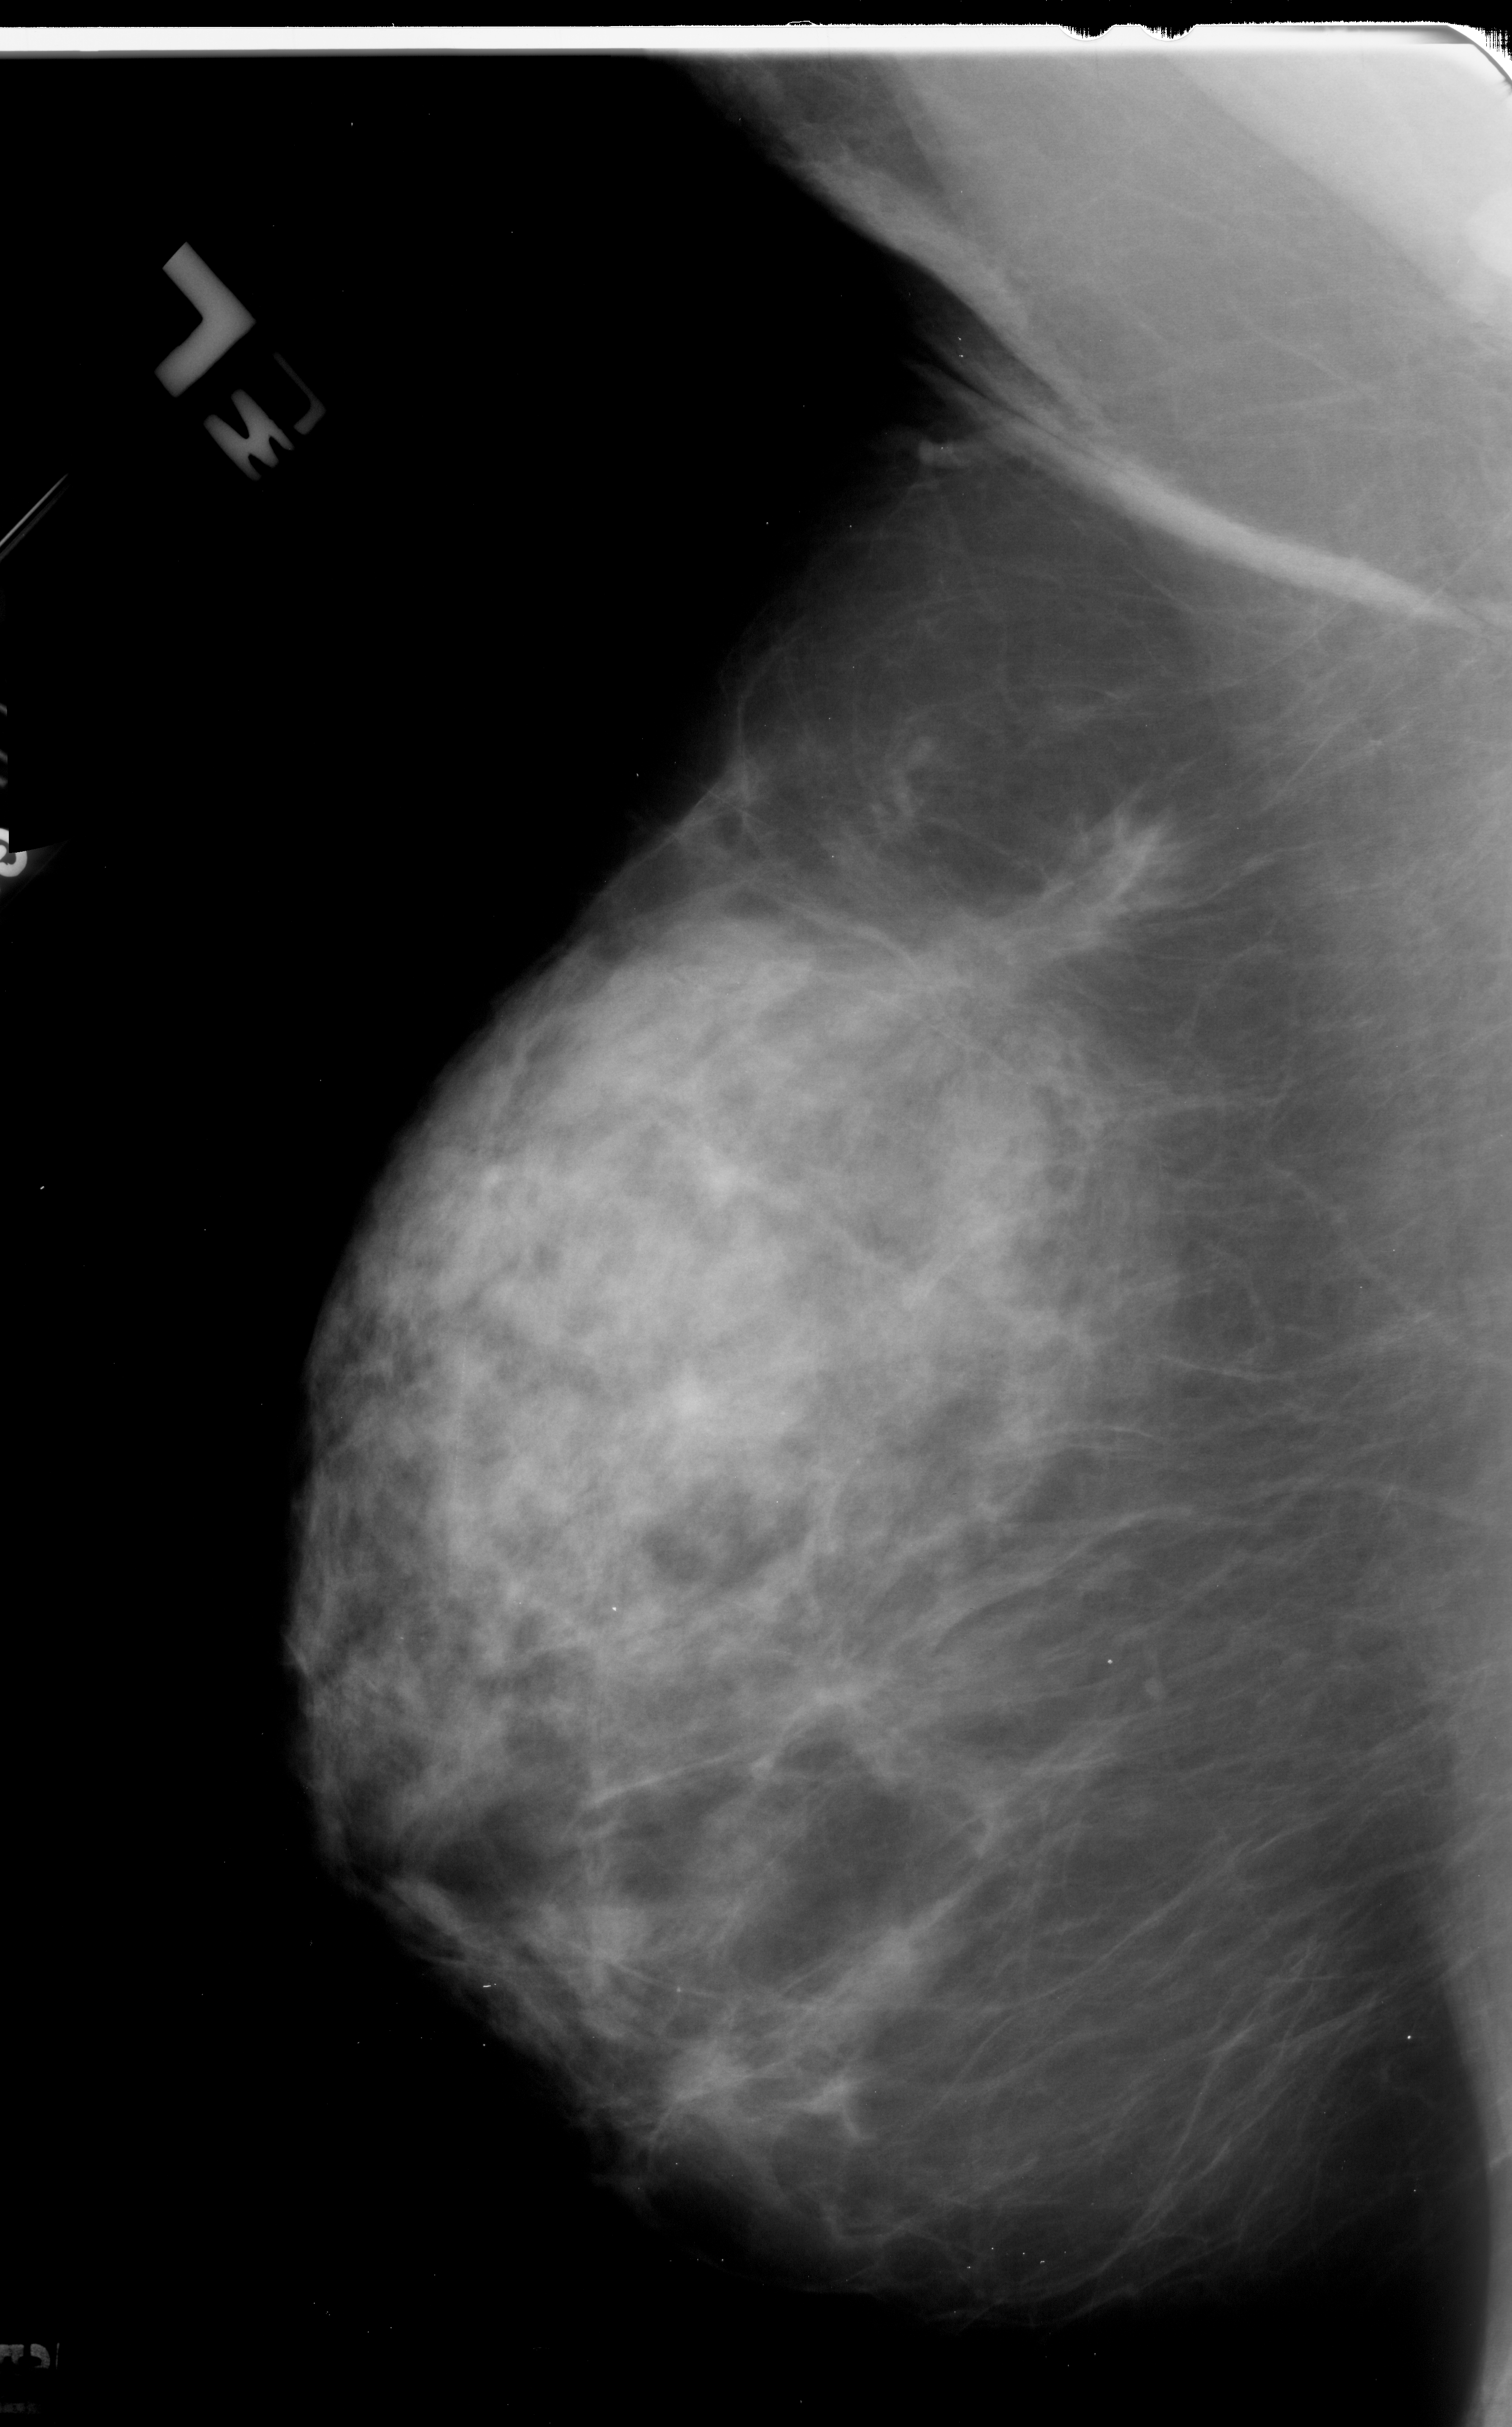
Scanned film-screen mammogram; left breast; MLO view.
- Finding: mass, shape architectural distortion, margins spiculated; BI-RADS assessment category 5; pathology (as recorded): malignant.